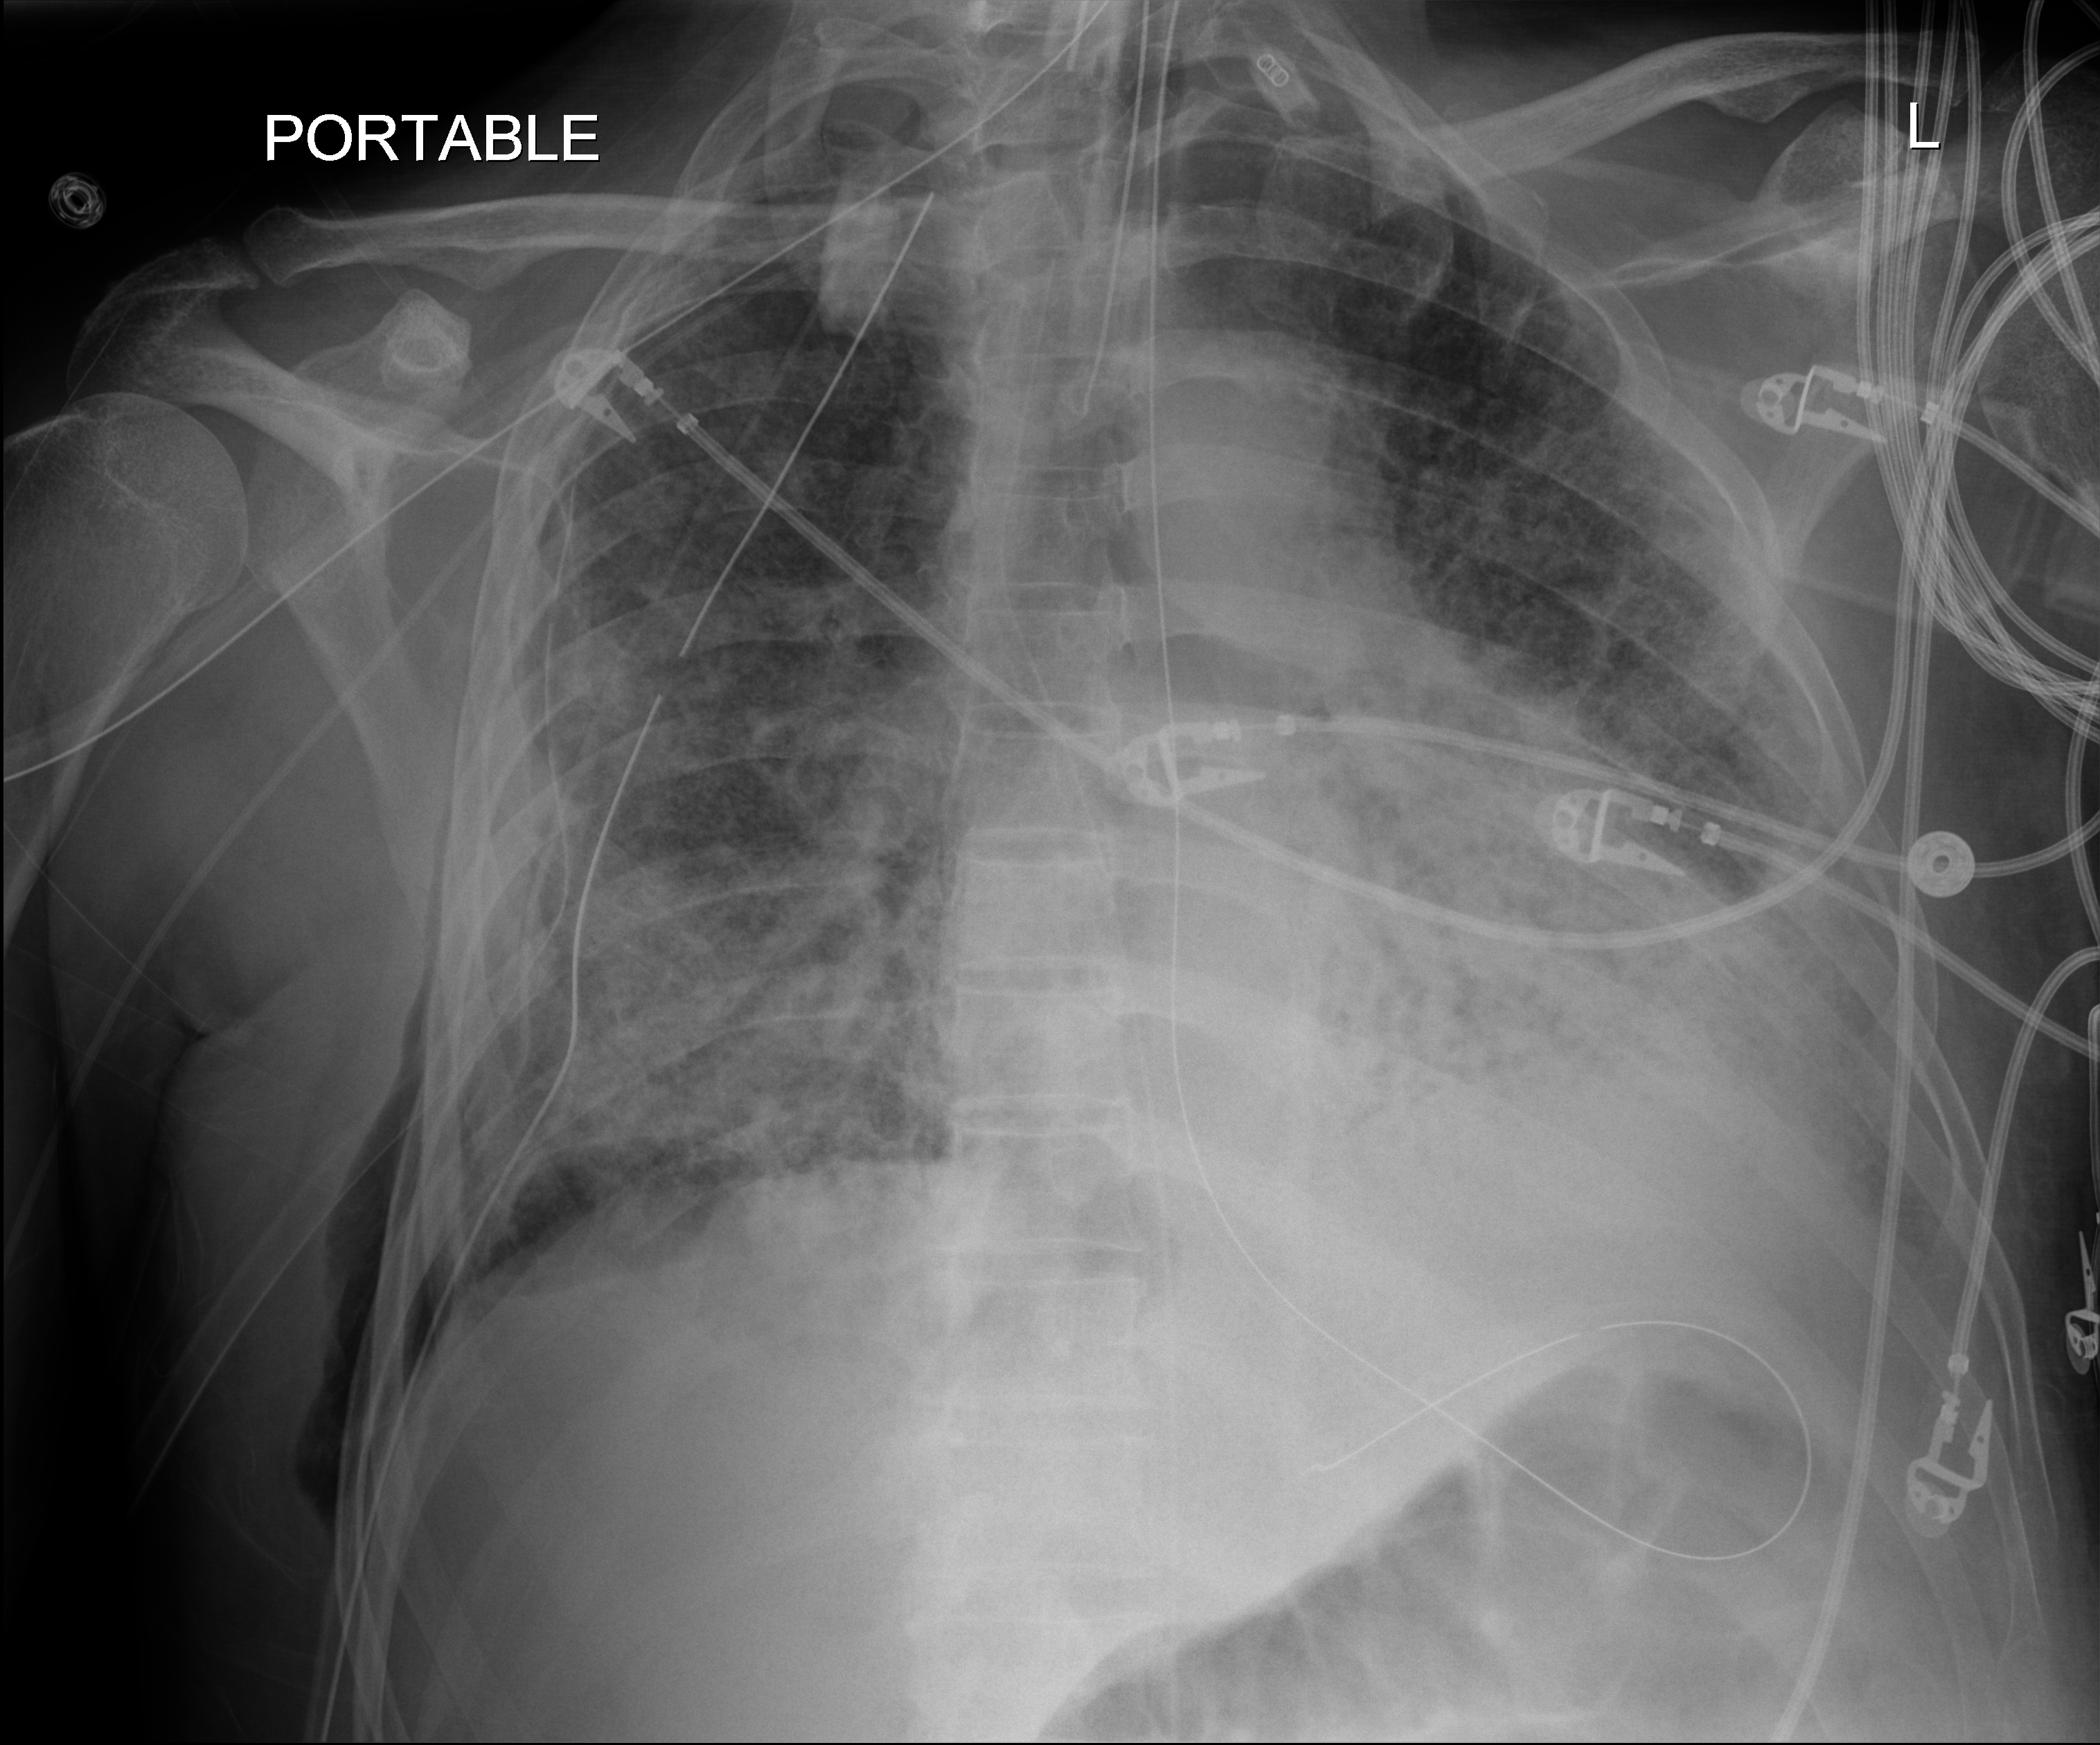
Portable chest radiograph. Male patient hospitalised with COVID-19, age 60–74 years.
Admission-level facts for this patient (not findings on this image; timing relative to this image not recorded): chronic kidney disease (admission record): no; admitted to intensive care during this hospital stay: yes; COPD (admission record): no.